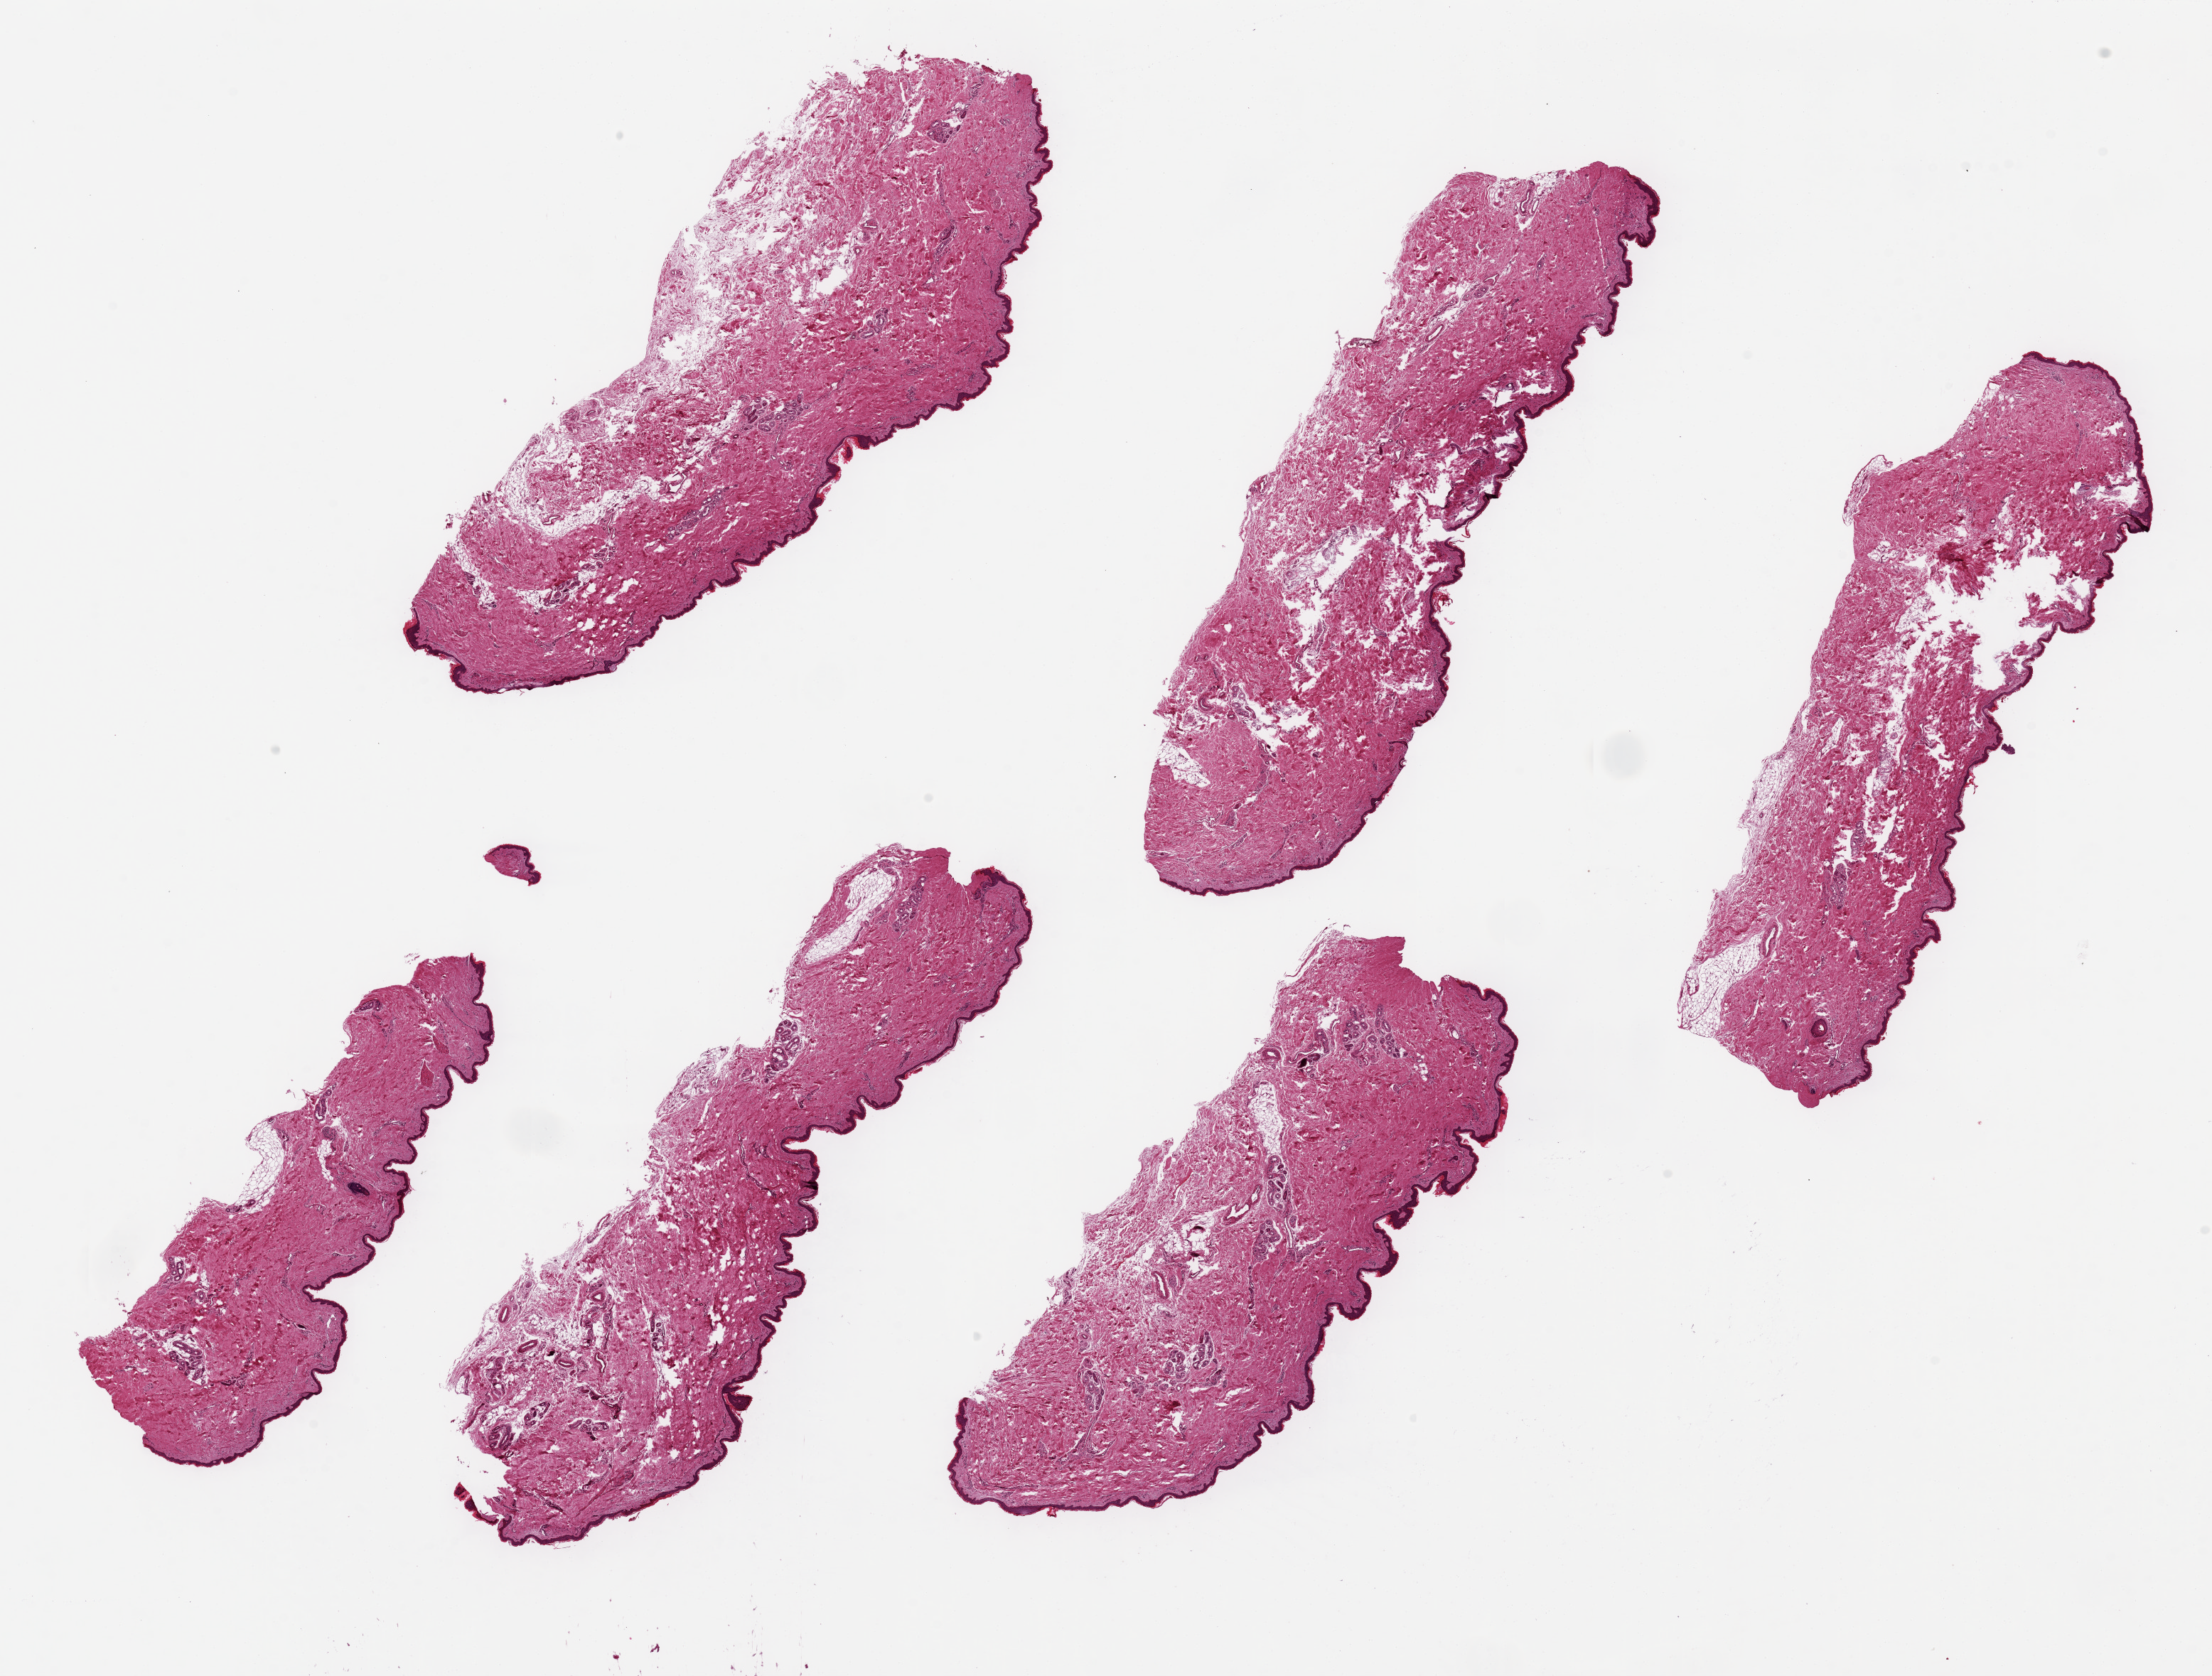
Haematoxylin and eosin whole-slide image, brightfield, a low-resolution overview of the entire scanned area, about 24.6 x 18.6 mm (slide scanned at 20x), PAXgene-fixed, paraffin-embedded tissue, sampled site (target tissue): skin of lower leg, donor tissue sample. Male donor.
Review note (as recorded): 6 pieces up to 9x3.6 mm.